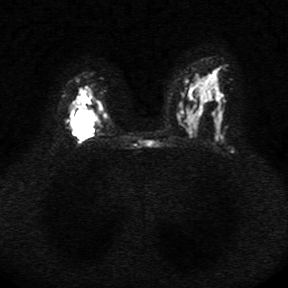
Breast MRI, one axial slice. Position 19 of 34 along the scan axis. Diffusion-weighted series; image 2 of 4 stored at this slice position (different b-values; order by instance number). 1.5 T. 5 mm slice thickness. 288 × 288 image matrix. Female patient.
Structures marked on this image (manually delineated by an expert):
- tumour on diffusion-weighted imaging: bounding box [x1, y1, x2, y2] px = [70, 109, 94, 136]